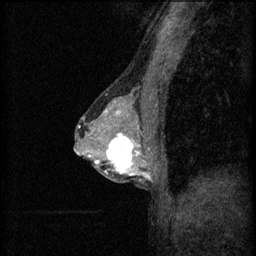
Breast MRI (dynamic contrast-enhanced), one sagittal slice. Slice 34 of 60 in the series (ordered by position). 3 images stored at this slice position (order not interpretable as contrast timing). 1.5 T. TE 4.2 ms, TR 8.2 ms. 256 × 256 image matrix. Female patient, age 44 years.
Structures marked on this image (semi-automatically segmented with operator editing):
- analysis volume of interest (the breast-tissue region the enhancement analysis was run in; not a lesion): box from (x=102, y=132) to (x=151, y=181) px
- tumour enhancement mask (voxels above the 70 % enhancement threshold inside the analysis volume of interest): (x=106, y=134)–(x=151, y=177)